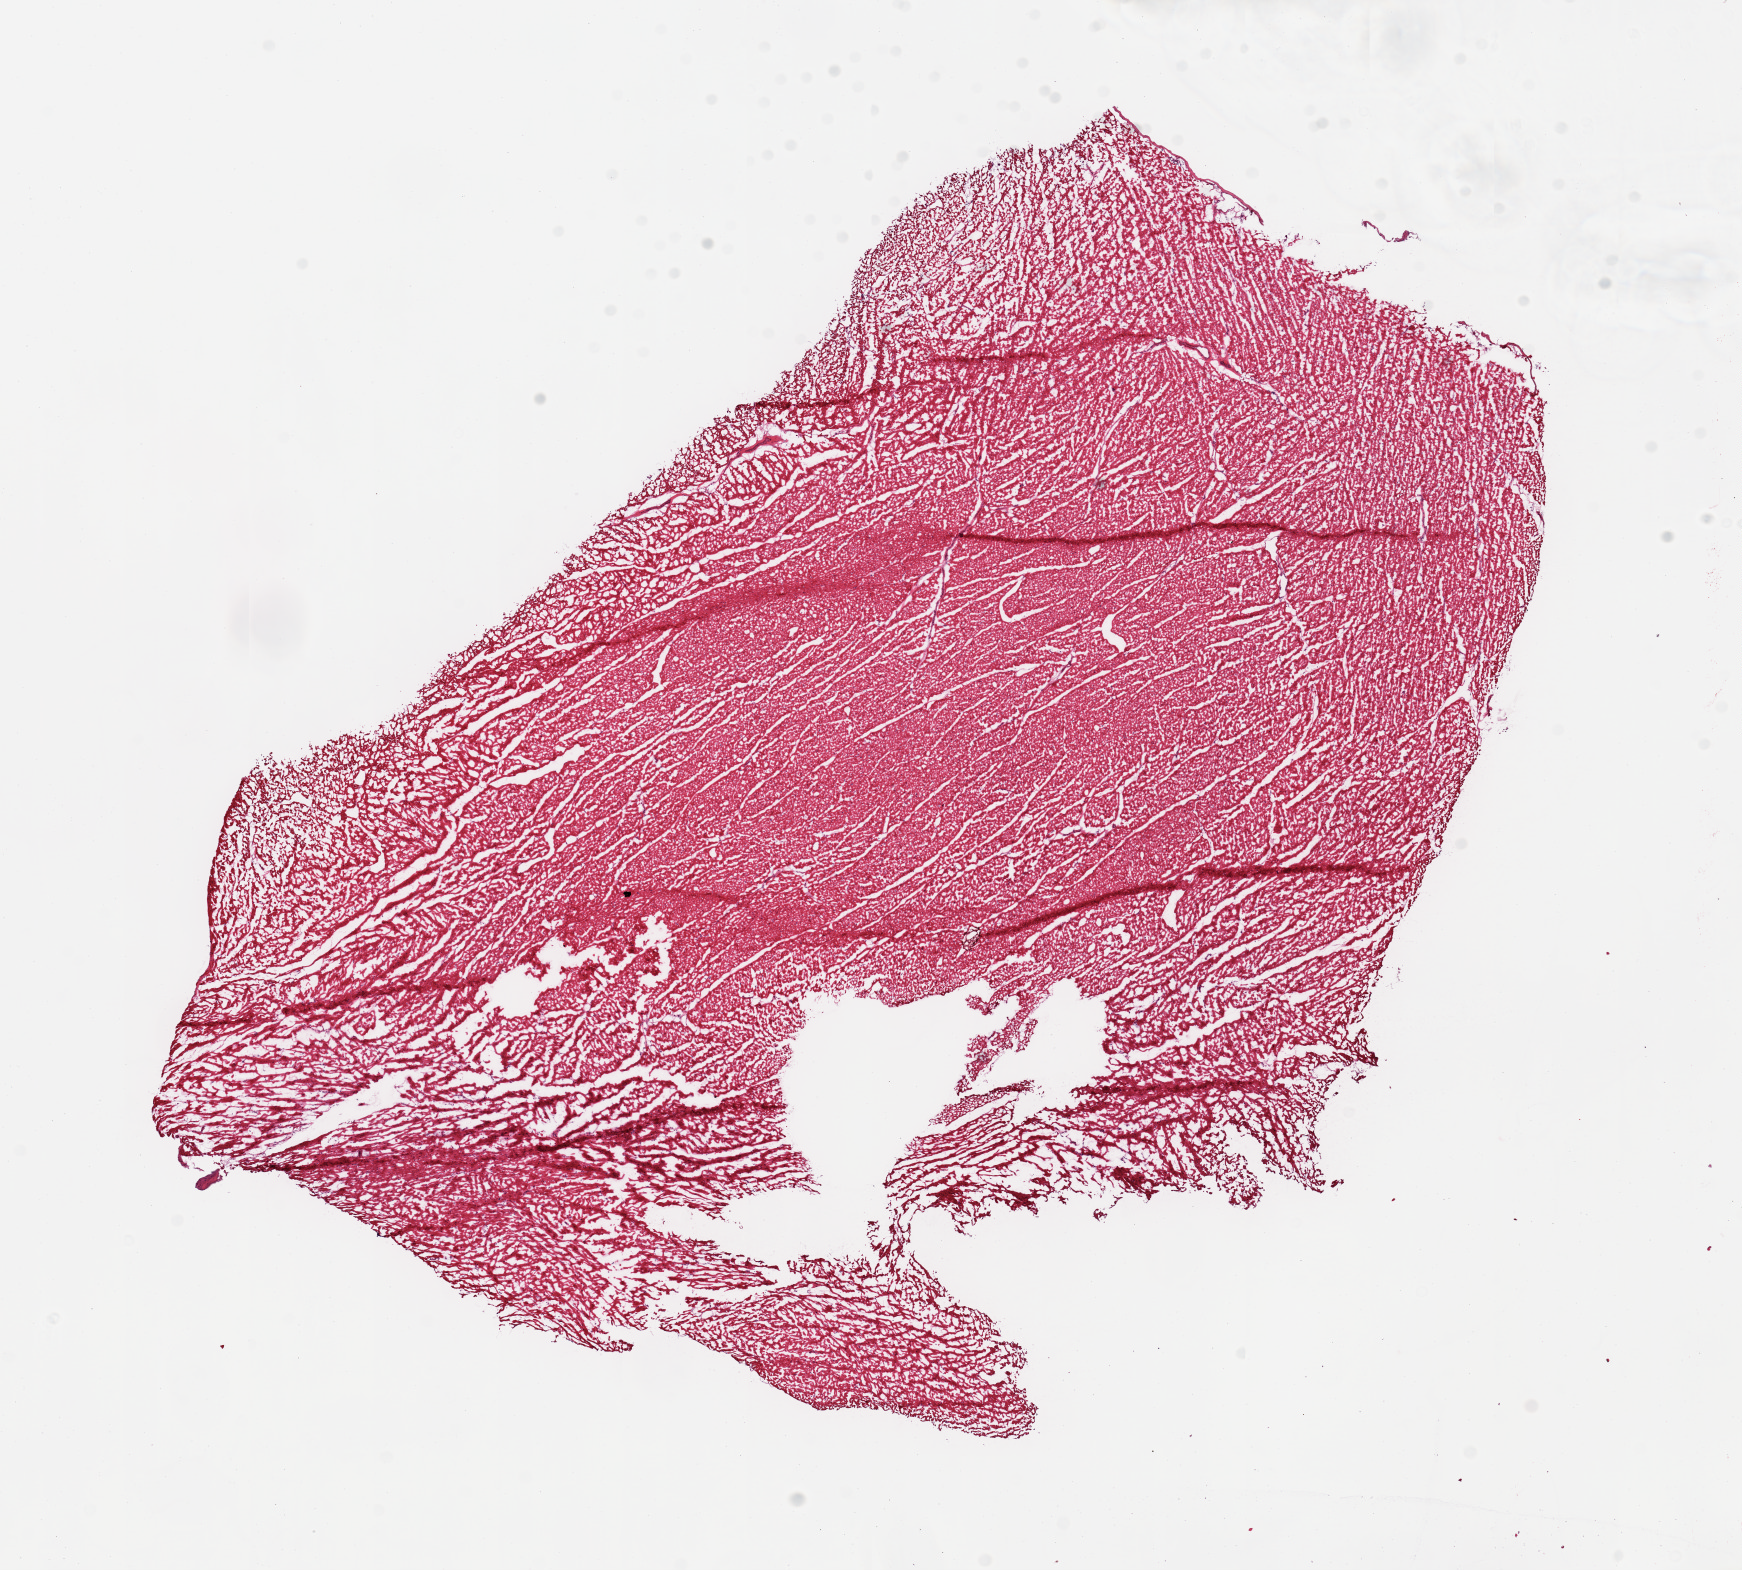
H&E whole-slide image — whole scanned area (about 13.8 x 12.4 mm) shown as a low-resolution overview, frozen section, target tissue: heart, tissue donor sample. Female donor.
• review note (as recorded): 1 piece